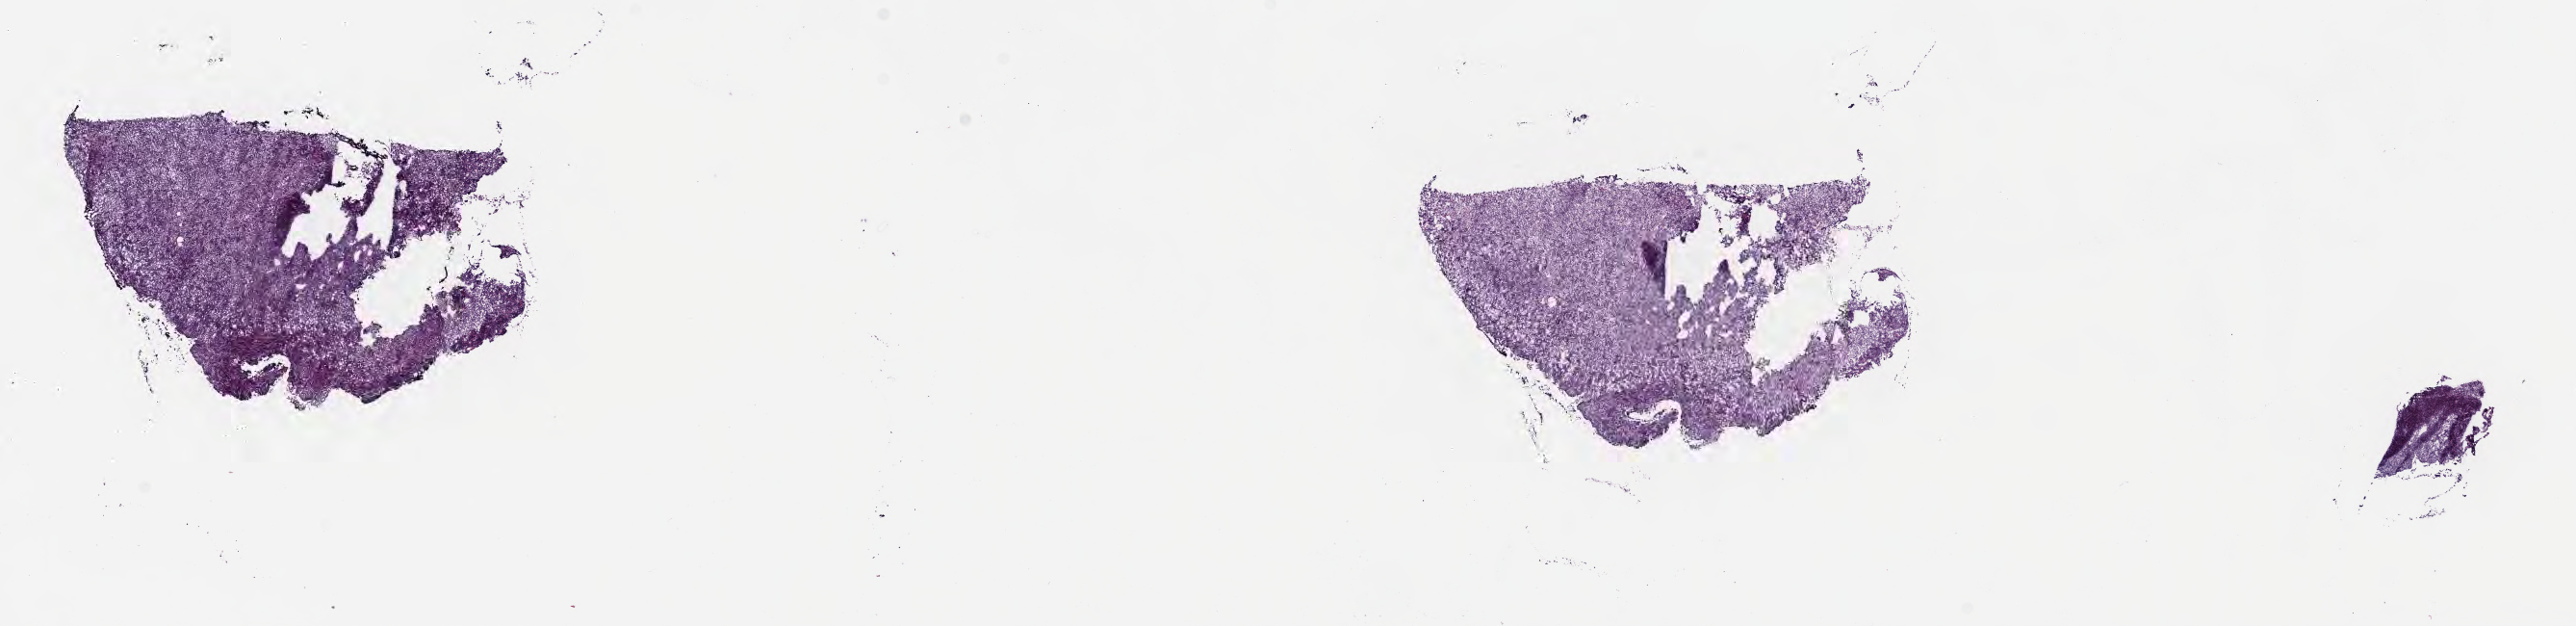
Digitized hematoxylin and eosin (H&E)-stained section — shown as a low-resolution overview of the whole scanned area (about 21.6 x 5.3 mm); cryosection; specimen: primary tumor; site: cranium. Patient: male, age at initial diagnosis 2 years. Slide review estimates, as recorded: tumor cells 85%, tumor nuclei 90%, stromal cells 10%, necrosis 5%, normal cells 0%. Infiltration values recorded for this section: lymphocyte infiltration 70%, monocyte infiltration 15%, neutrophil infiltration 0%.
• diagnosis: Burkitt lymphoma, NOS
• Ann Arbor stage (patient): Stage IV